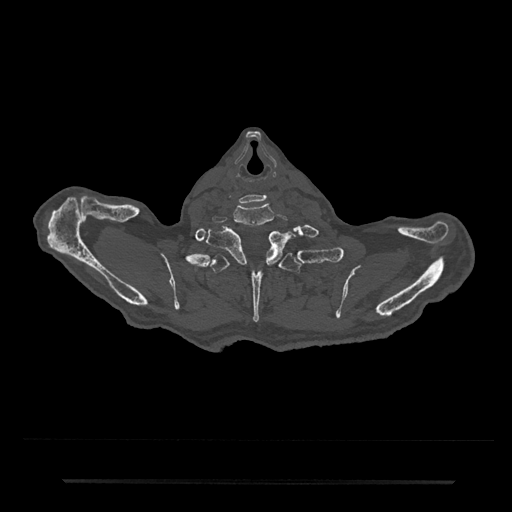
CT including the spine, one axial slice; position 715 of 797 along the scan axis; 120 kVp; bone window (W 1800 / L 400 HU); 512 × 512 image matrix. Male patient, age 74 years. From the clinical record (not read from this slice): primary cancer: prostate.
Outlined on this slice (semi-automatically segmented with operator editing):
- T1 vertebra: box from (x=207, y=229) to (x=291, y=266) px
- T2 vertebra: (x=201, y=250)–(x=307, y=323)